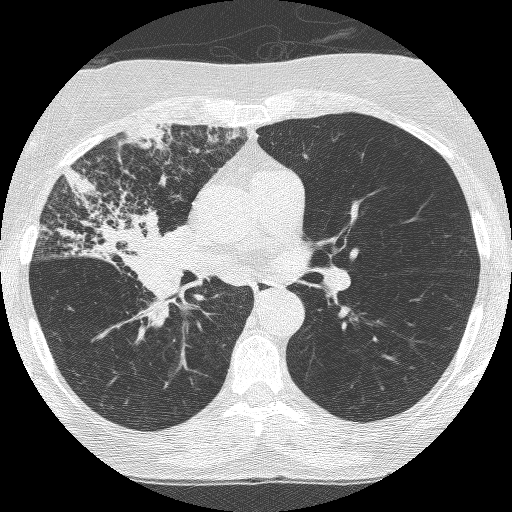
Low-dose screening chest CT, axial slice. Third screening round (two years after baseline). Lung window (W 1500 / L -600 HU). 1.25 mm slice thickness. Lung (sharp) reconstruction kernel (BONE). Slice 144 of 253 in the series. 512 × 512 image matrix. Female participant, aged 64 years at enrolment. Former smoker at enrolment.
Lesion marked by an expert reader, bounding box <65,178,201,316> (left, top, right, bottom; pixels). Reader record for this screening exam (exam-level; its link to the box is not recorded): non-calcified nodule or mass ≥4 mm, right upper lobe, 49 × 43 mm, spiculated (stellate) margins, soft tissue attenuation, pre-existing on the prior screen: yes; interval growth: yes.